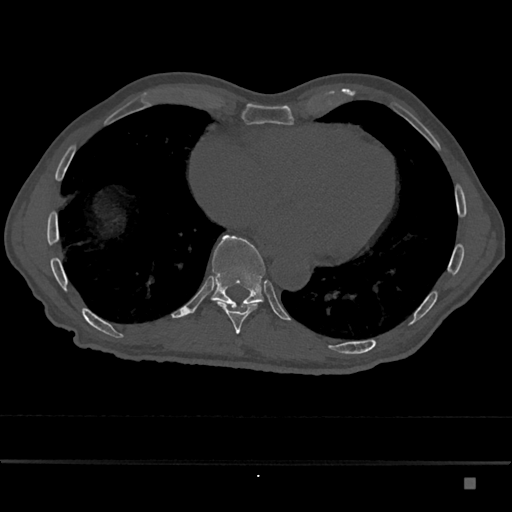
CT including the spine, one axial slice. Position 776 of 797 along the scan axis. Reconstruction kernel Br40s/3. Bone window (W 1800 / L 400 HU). 0.5 mm slice thickness. 512 × 512 image matrix, field of view 390 × 390 mm. Patient: male, 72 years. From the clinical record (not read from this slice): primary cancer: prostate.
Outlined on this slice (semi-automatic segmentation, software-assisted and operator-edited):
- T10 vertebra: bounding box (x1, y1, x2, y2) in pixels: (210, 235, 266, 310)
- T9 vertebra: (219, 303, 257, 334)